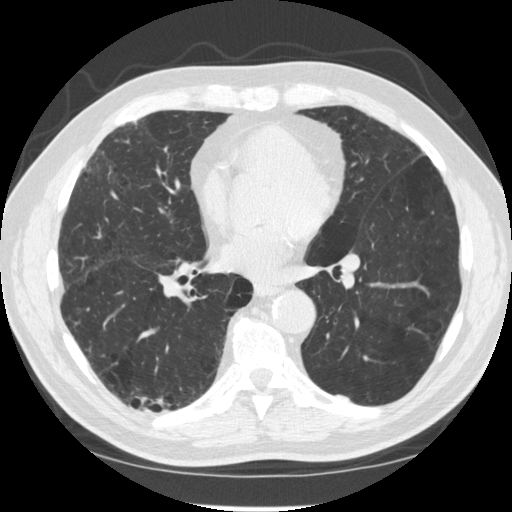
Chest CT (low-dose screening protocol), one axial image. Second annual screen. Lung window (W 1500 / L -600 HU). 512 × 512 image matrix. Male participant, aged 70 years at enrolment.
• Expert reader's lesion annotation, box from (x=126, y=377) to (x=177, y=431) px.
• The screening reader recorded 2 non-calcified nodules or masses ≥4 mm on this exam (right lower lobe, right lower lobe); which of them this box marks is not recorded.
• Later outcome: lung cancer diagnosed 617 days after this screen (after the third annual screen) — squamous cell carcinoma, NOS, right upper lobe, poorly differentiated (G3), stage IV (AJCC 6th edition).